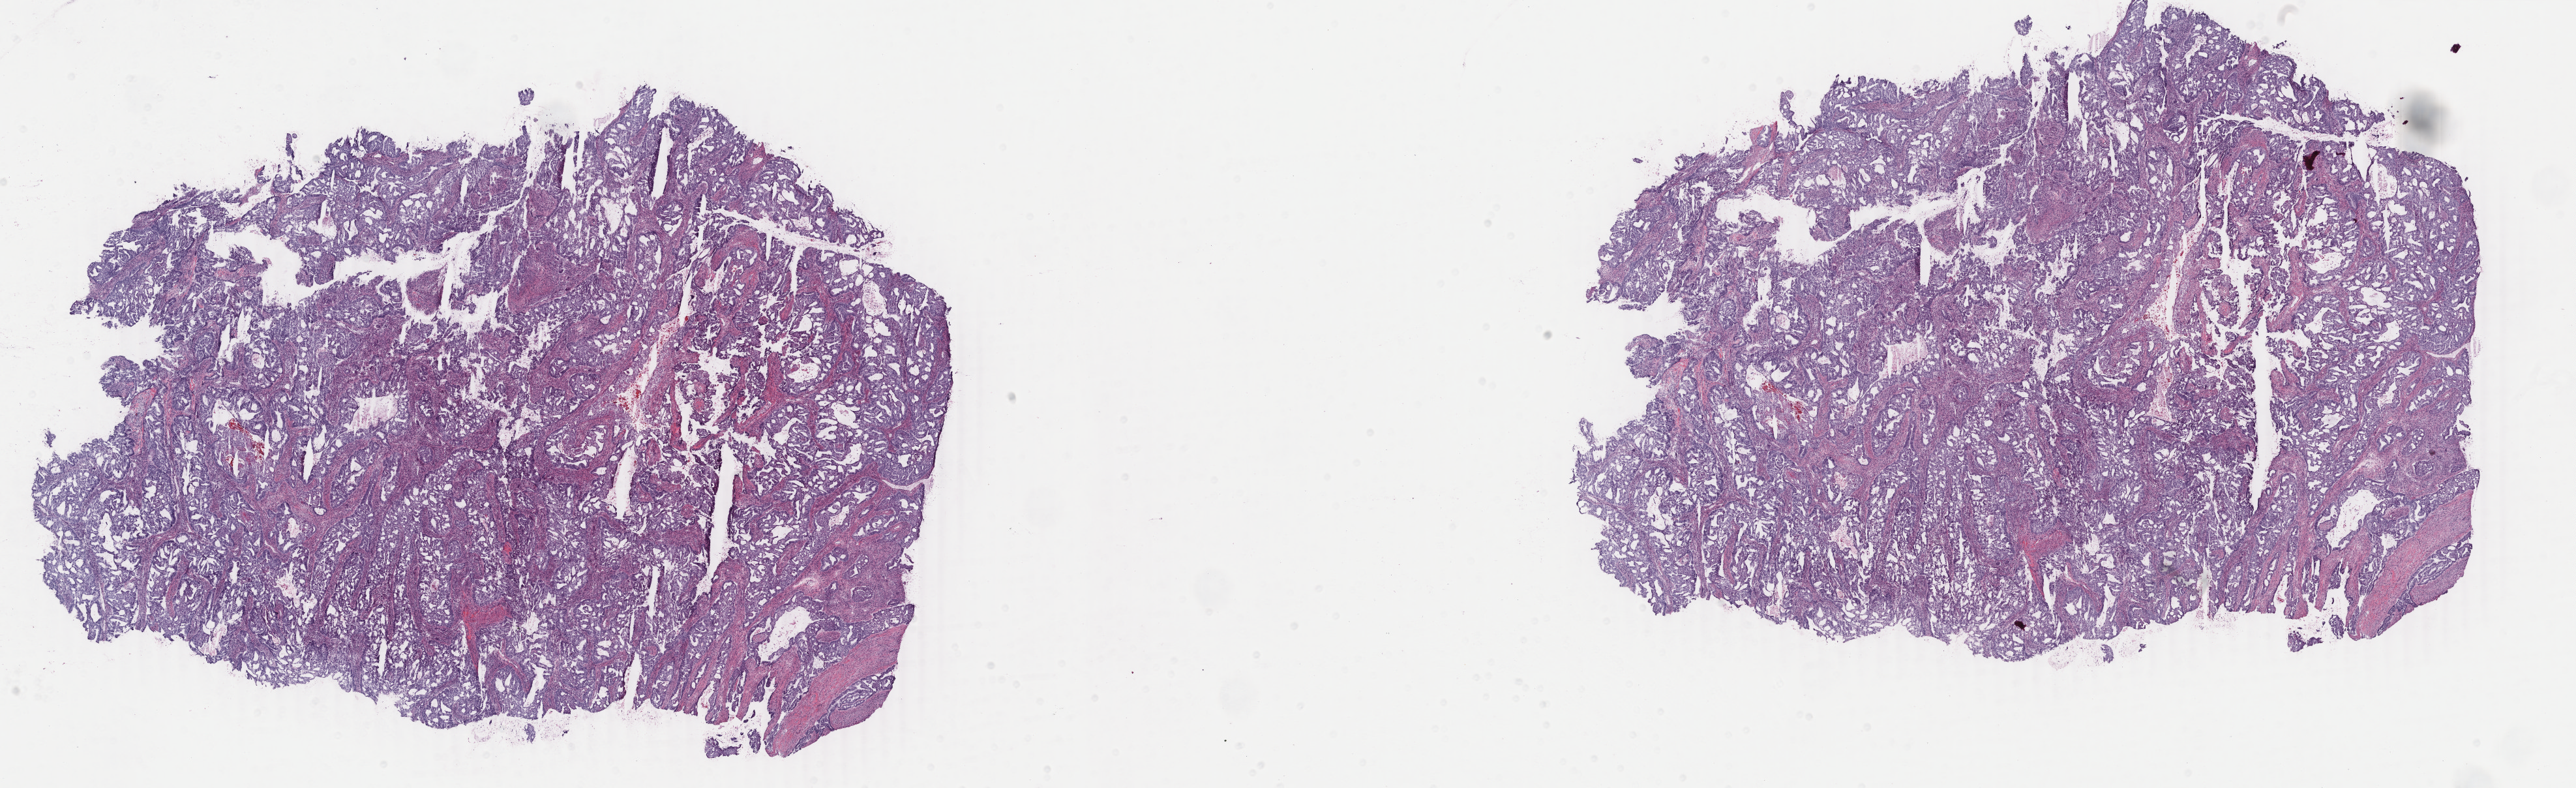
Whole-slide histology image, H&E-stained — low-resolution overview of the scanned area, about 31.4 x 9.6 mm (from a 40x scan), frozen section, primary tumour sample from the uterus. Patient: female, age at initial diagnosis 60 years. Histologic grade: G2 (moderately differentiated). Composition of this section per pathologist review: tumour cells 70%, tumour nuclei 70%, normal cells 15%, stromal cells 14%, necrosis 1%. Infiltration values recorded for this section: lymphocyte infiltration 5%, monocyte infiltration 1%, neutrophil infiltration 0%.
- pathologic diagnosis: Endometrioid adenocarcinoma, NOS (endometrium)
- FIGO stage: IIIC